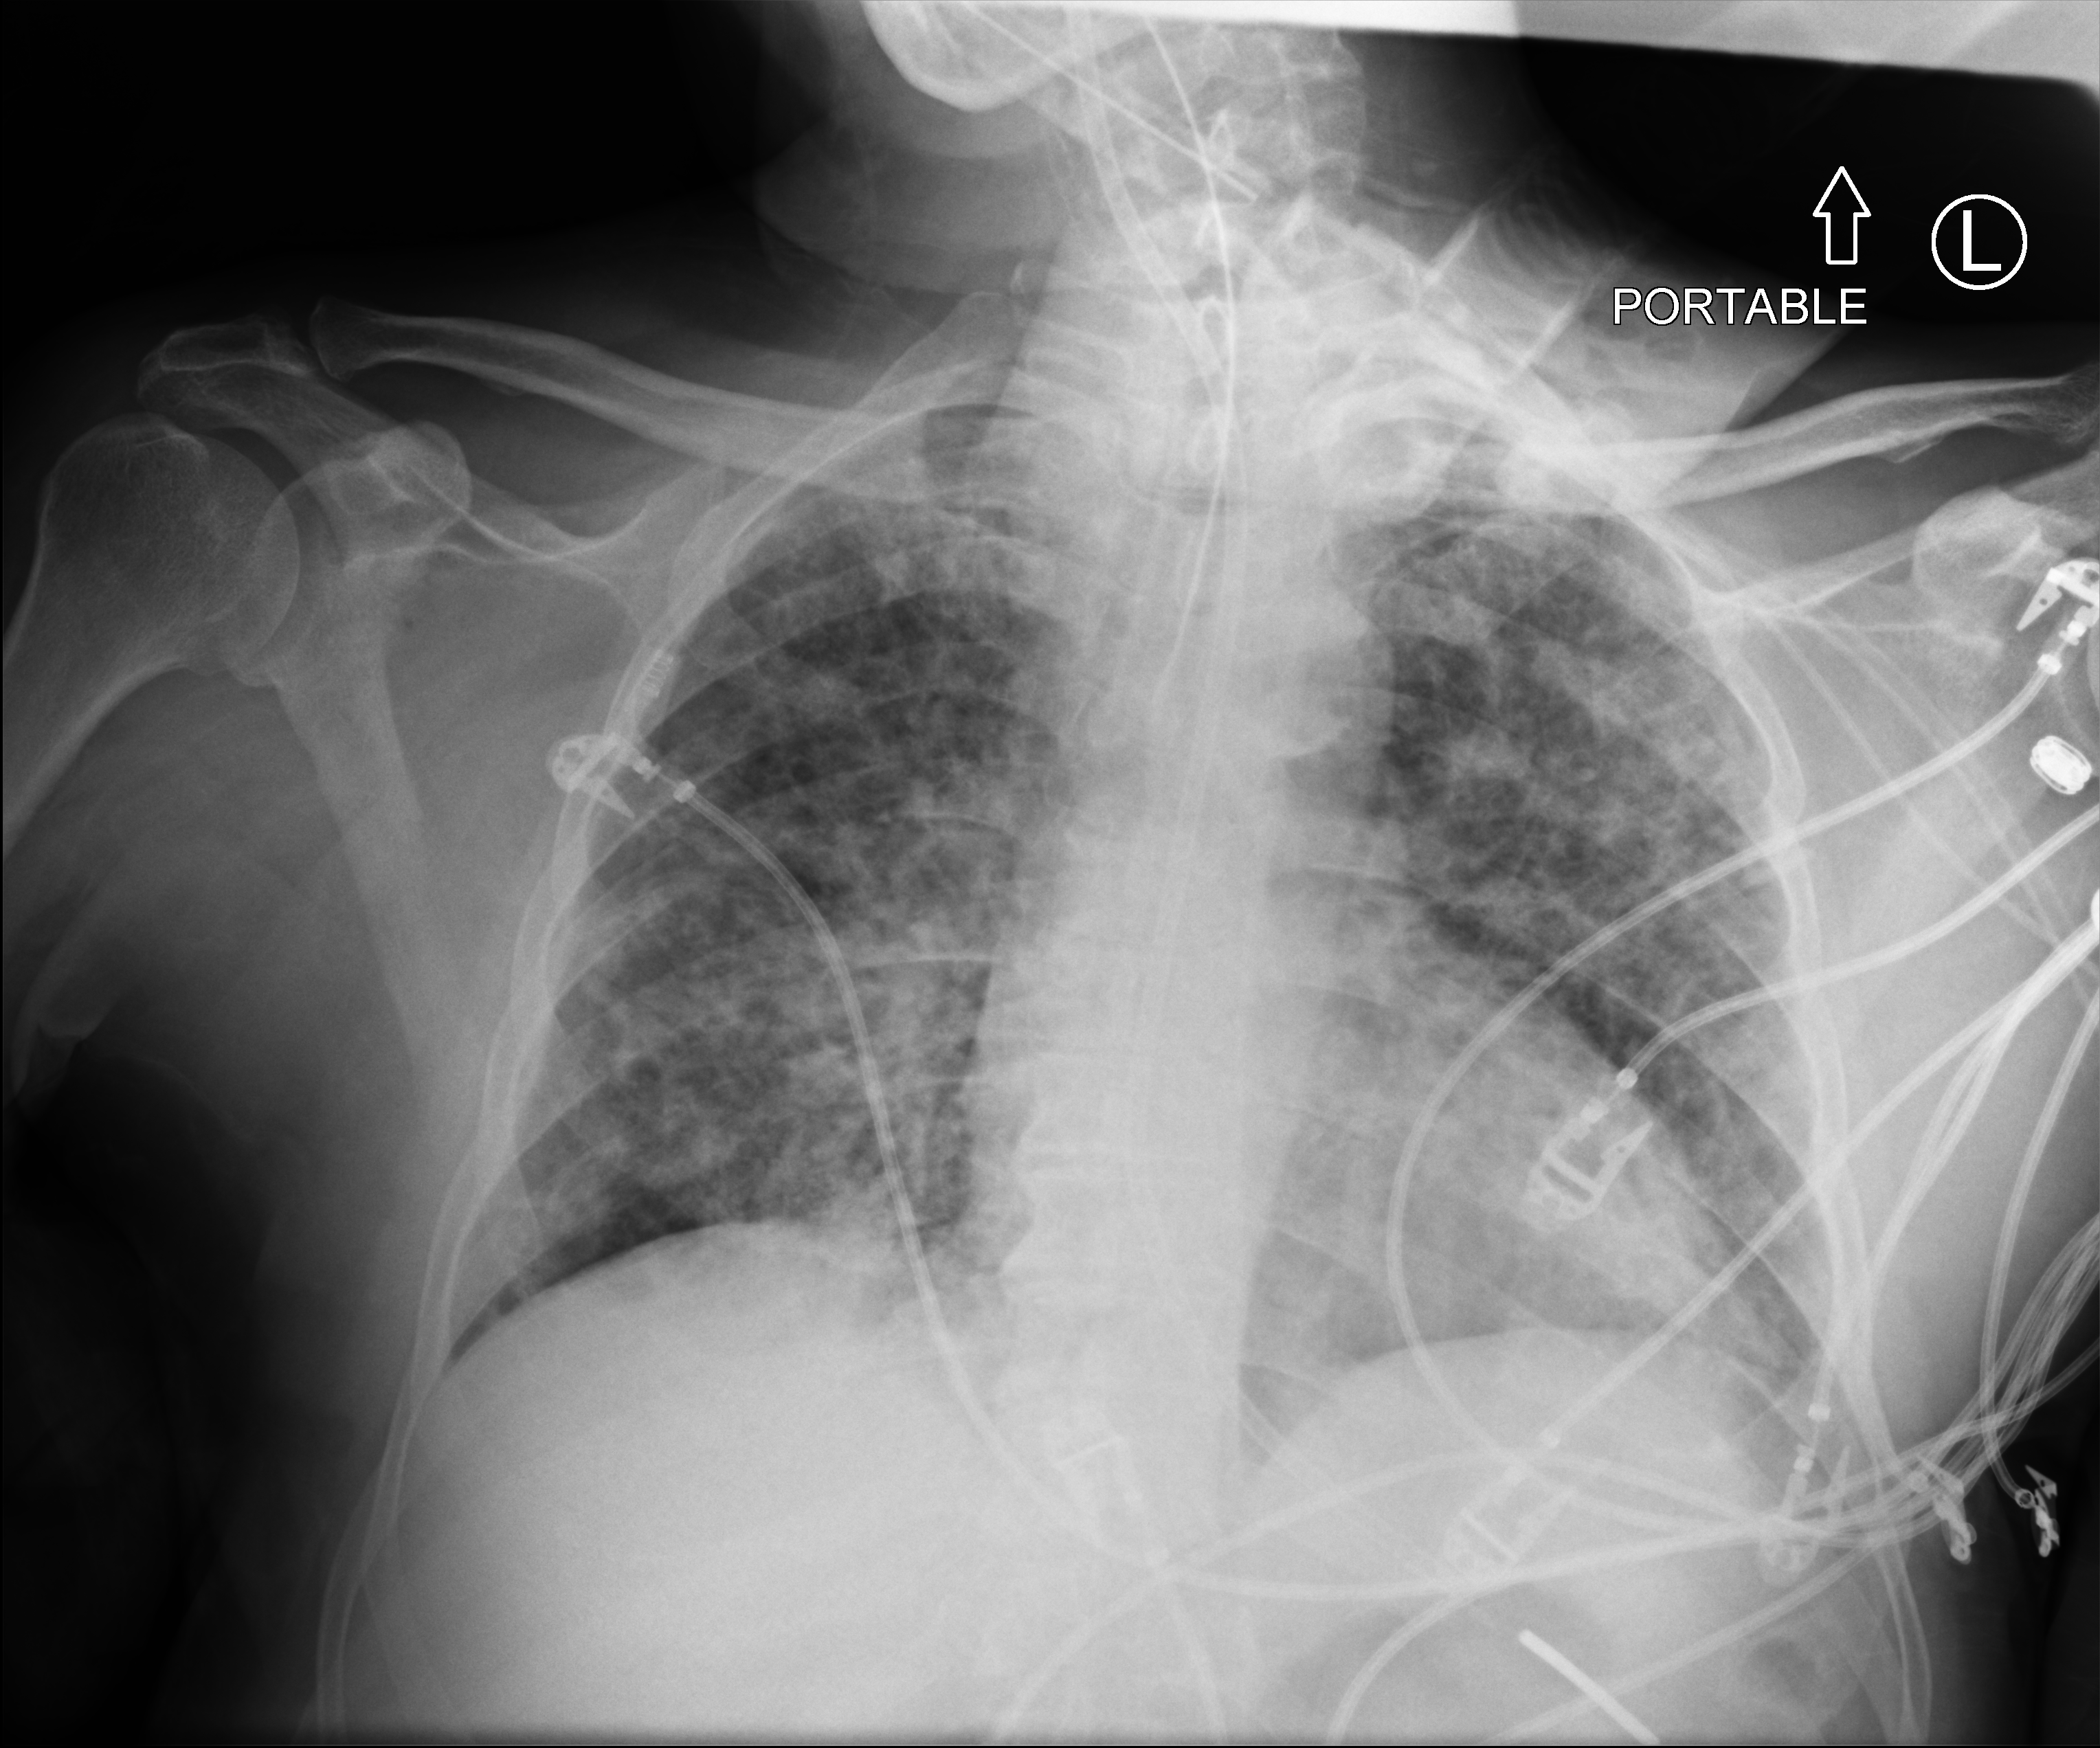
Portable chest radiograph, anteroposterior (AP) projection. Male patient hospitalised with COVID-19, age 18–59 years.
Admission-level facts for this patient (not findings on this image; timing relative to this image not recorded): length of hospital stay: 32 days; mechanically ventilated during this hospital stay: yes; chronic kidney disease (admission record): no.